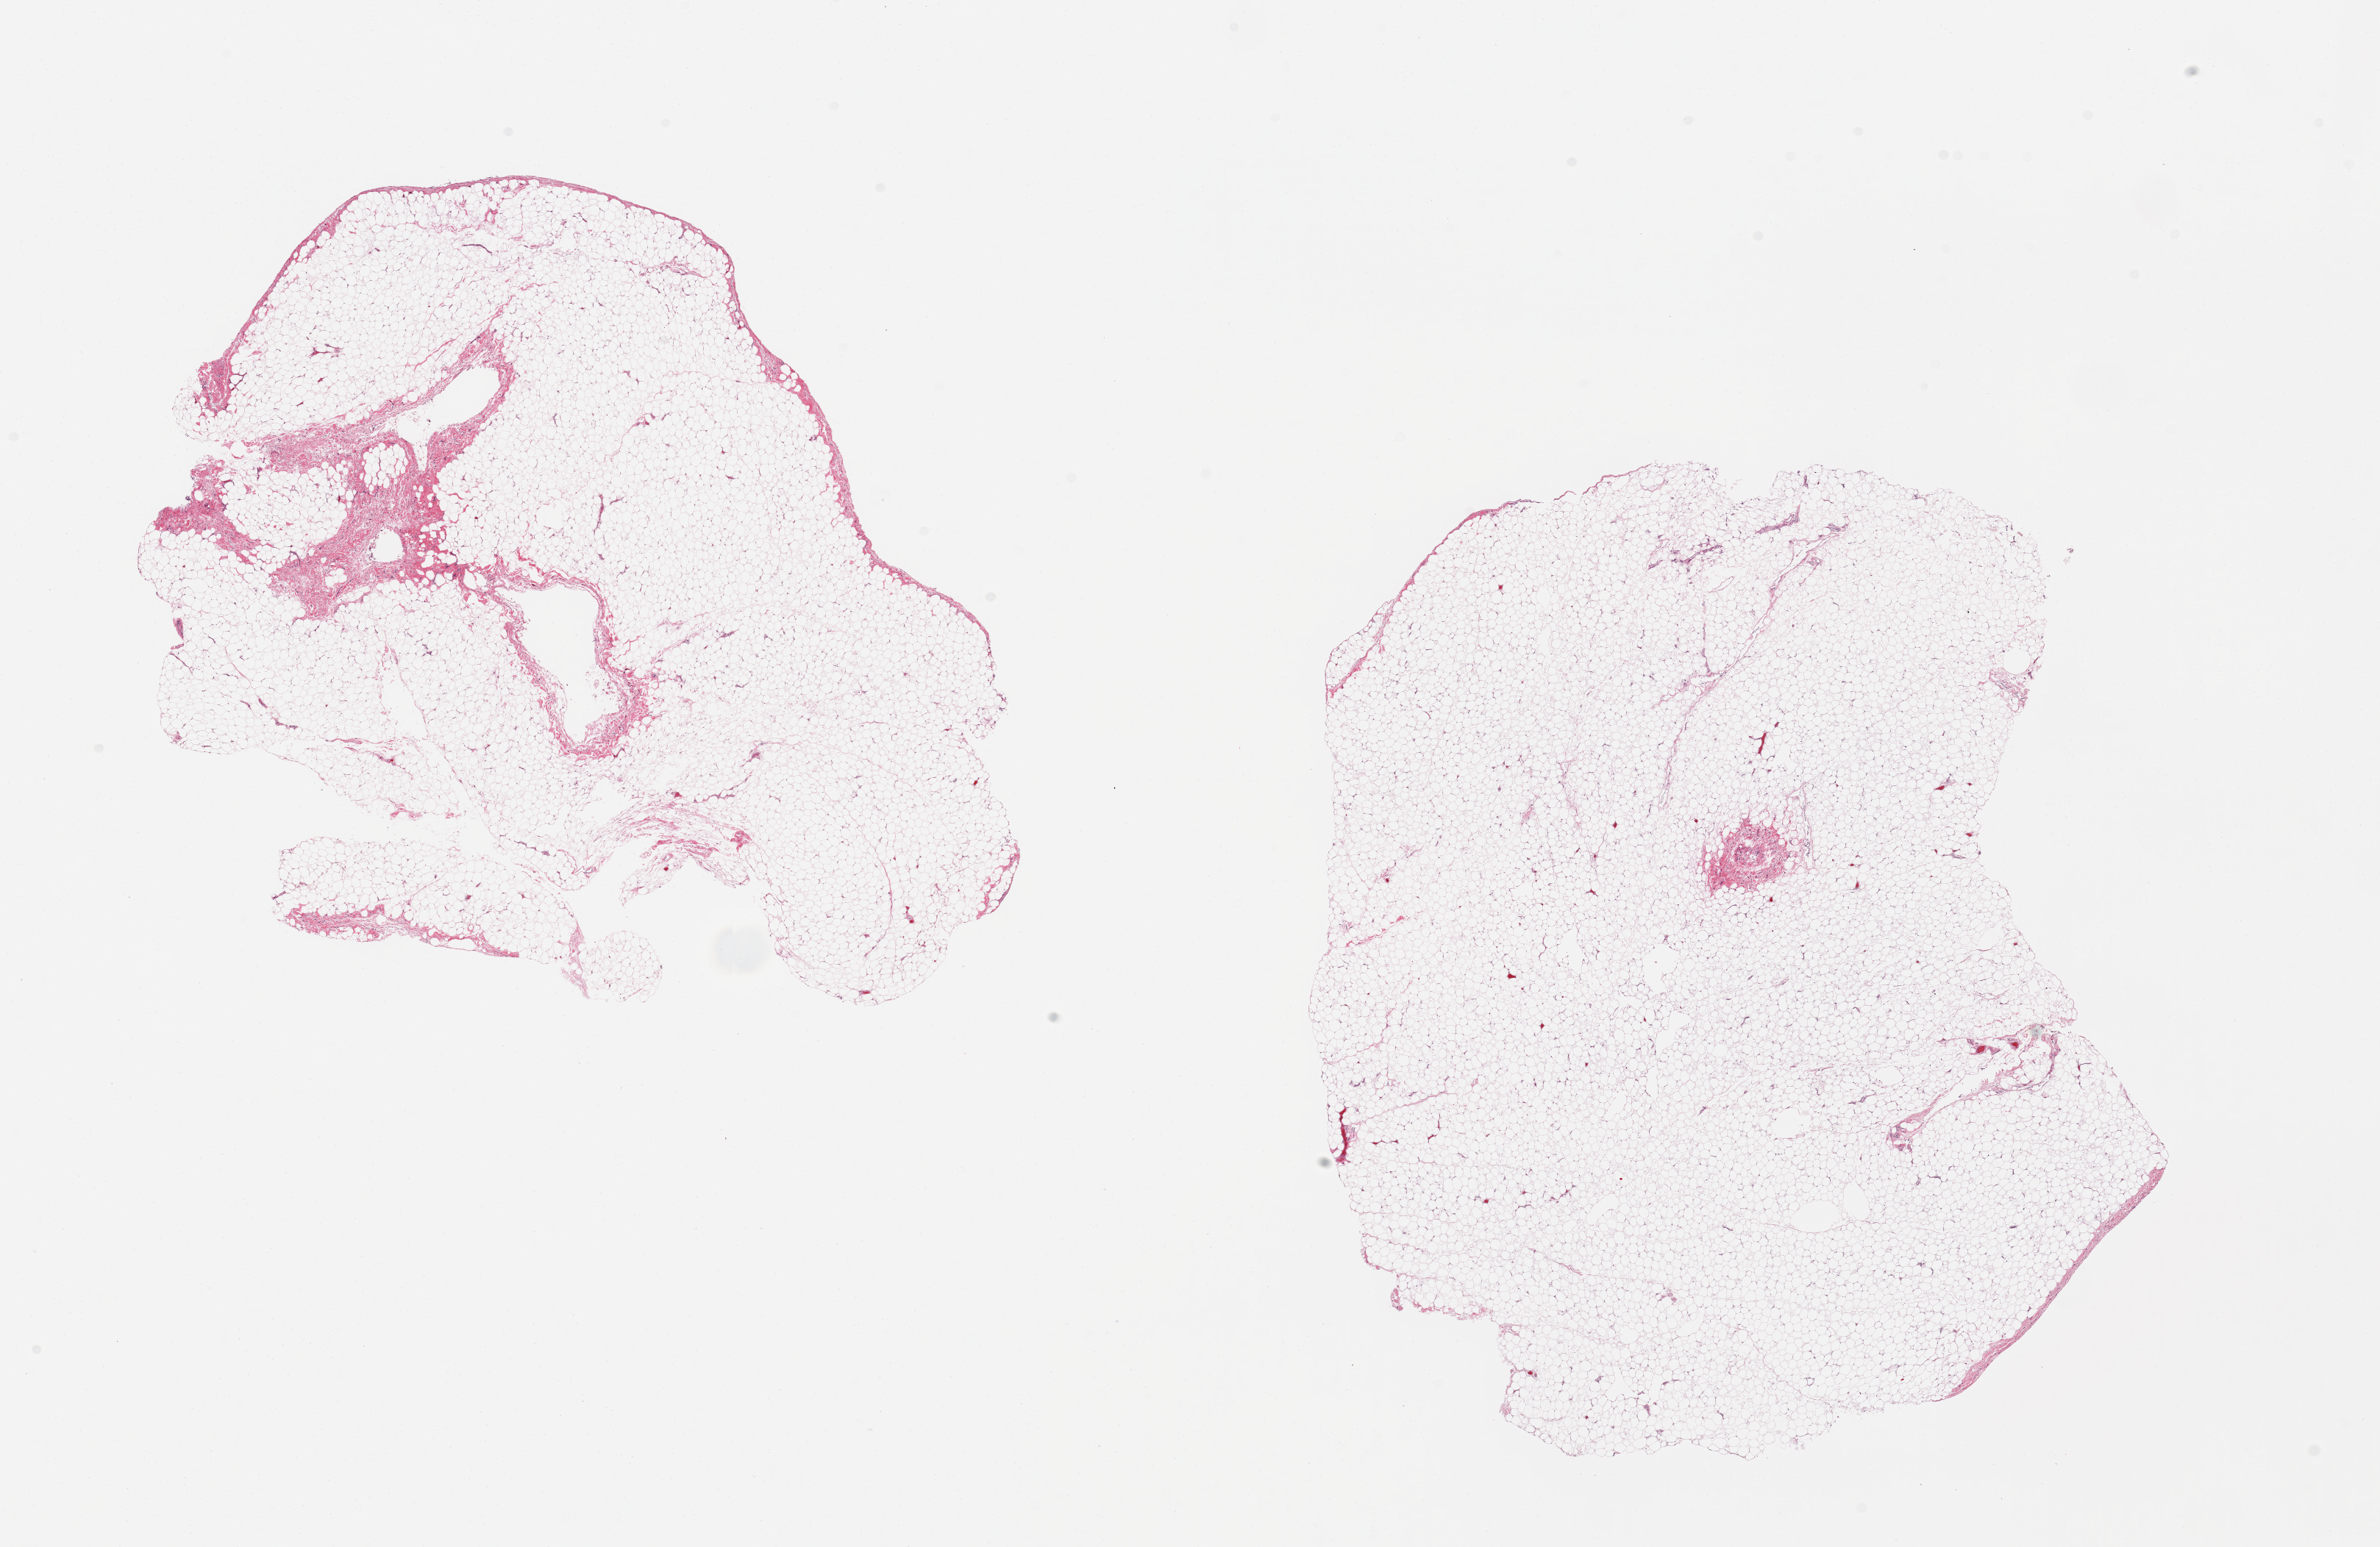
Haematoxylin and eosin whole-slide image — shown as a low-resolution overview of the whole scanned area (about 25.6 x 16.6 mm, slide scanned at 20x). PAXgene-fixed paraffin-embedded (PFPE) section. Sampled site (target tissue): omentum. Tissue donor sample. Male donor.
Review note (as recorded): 2 pieces; 10% & <5% fibrous component.